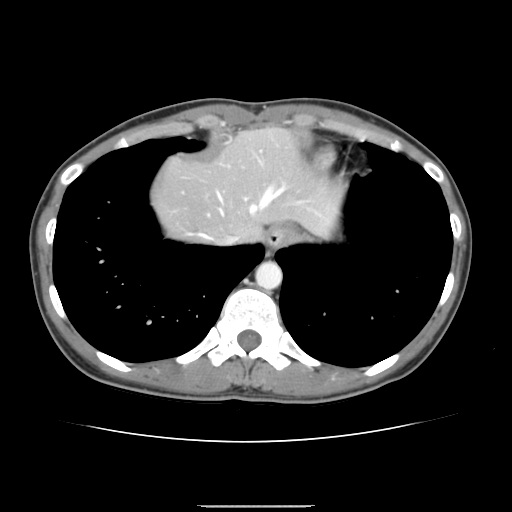
Contrast-enhanced abdominal CT, one axial slice; slice 128 of 150 in the series (ordered by position); 120 kVp; intravenous contrast given; soft-tissue window (W 400 / L 40 HU); 2.5 mm slice thickness; 512 × 512 image matrix, field of view 324 × 324 mm. Female patient, age 32 years. From the clinical record (not read from this slice): diagnosis: colorectal cancer liver metastases, imaged before liver resection; multiple liver metastases: yes; largest metastasis: 0.7 cm; disease in both lobes: no.
Outlined on this slice (manually delineated by an expert):
- hepatic veins: bounding box [x1, y1, x2, y2] px = [201, 187, 285, 243]
- liver: [154, 128, 340, 243]
- planned liver remnant (the part of the liver to remain after resection): [154, 128, 340, 242]